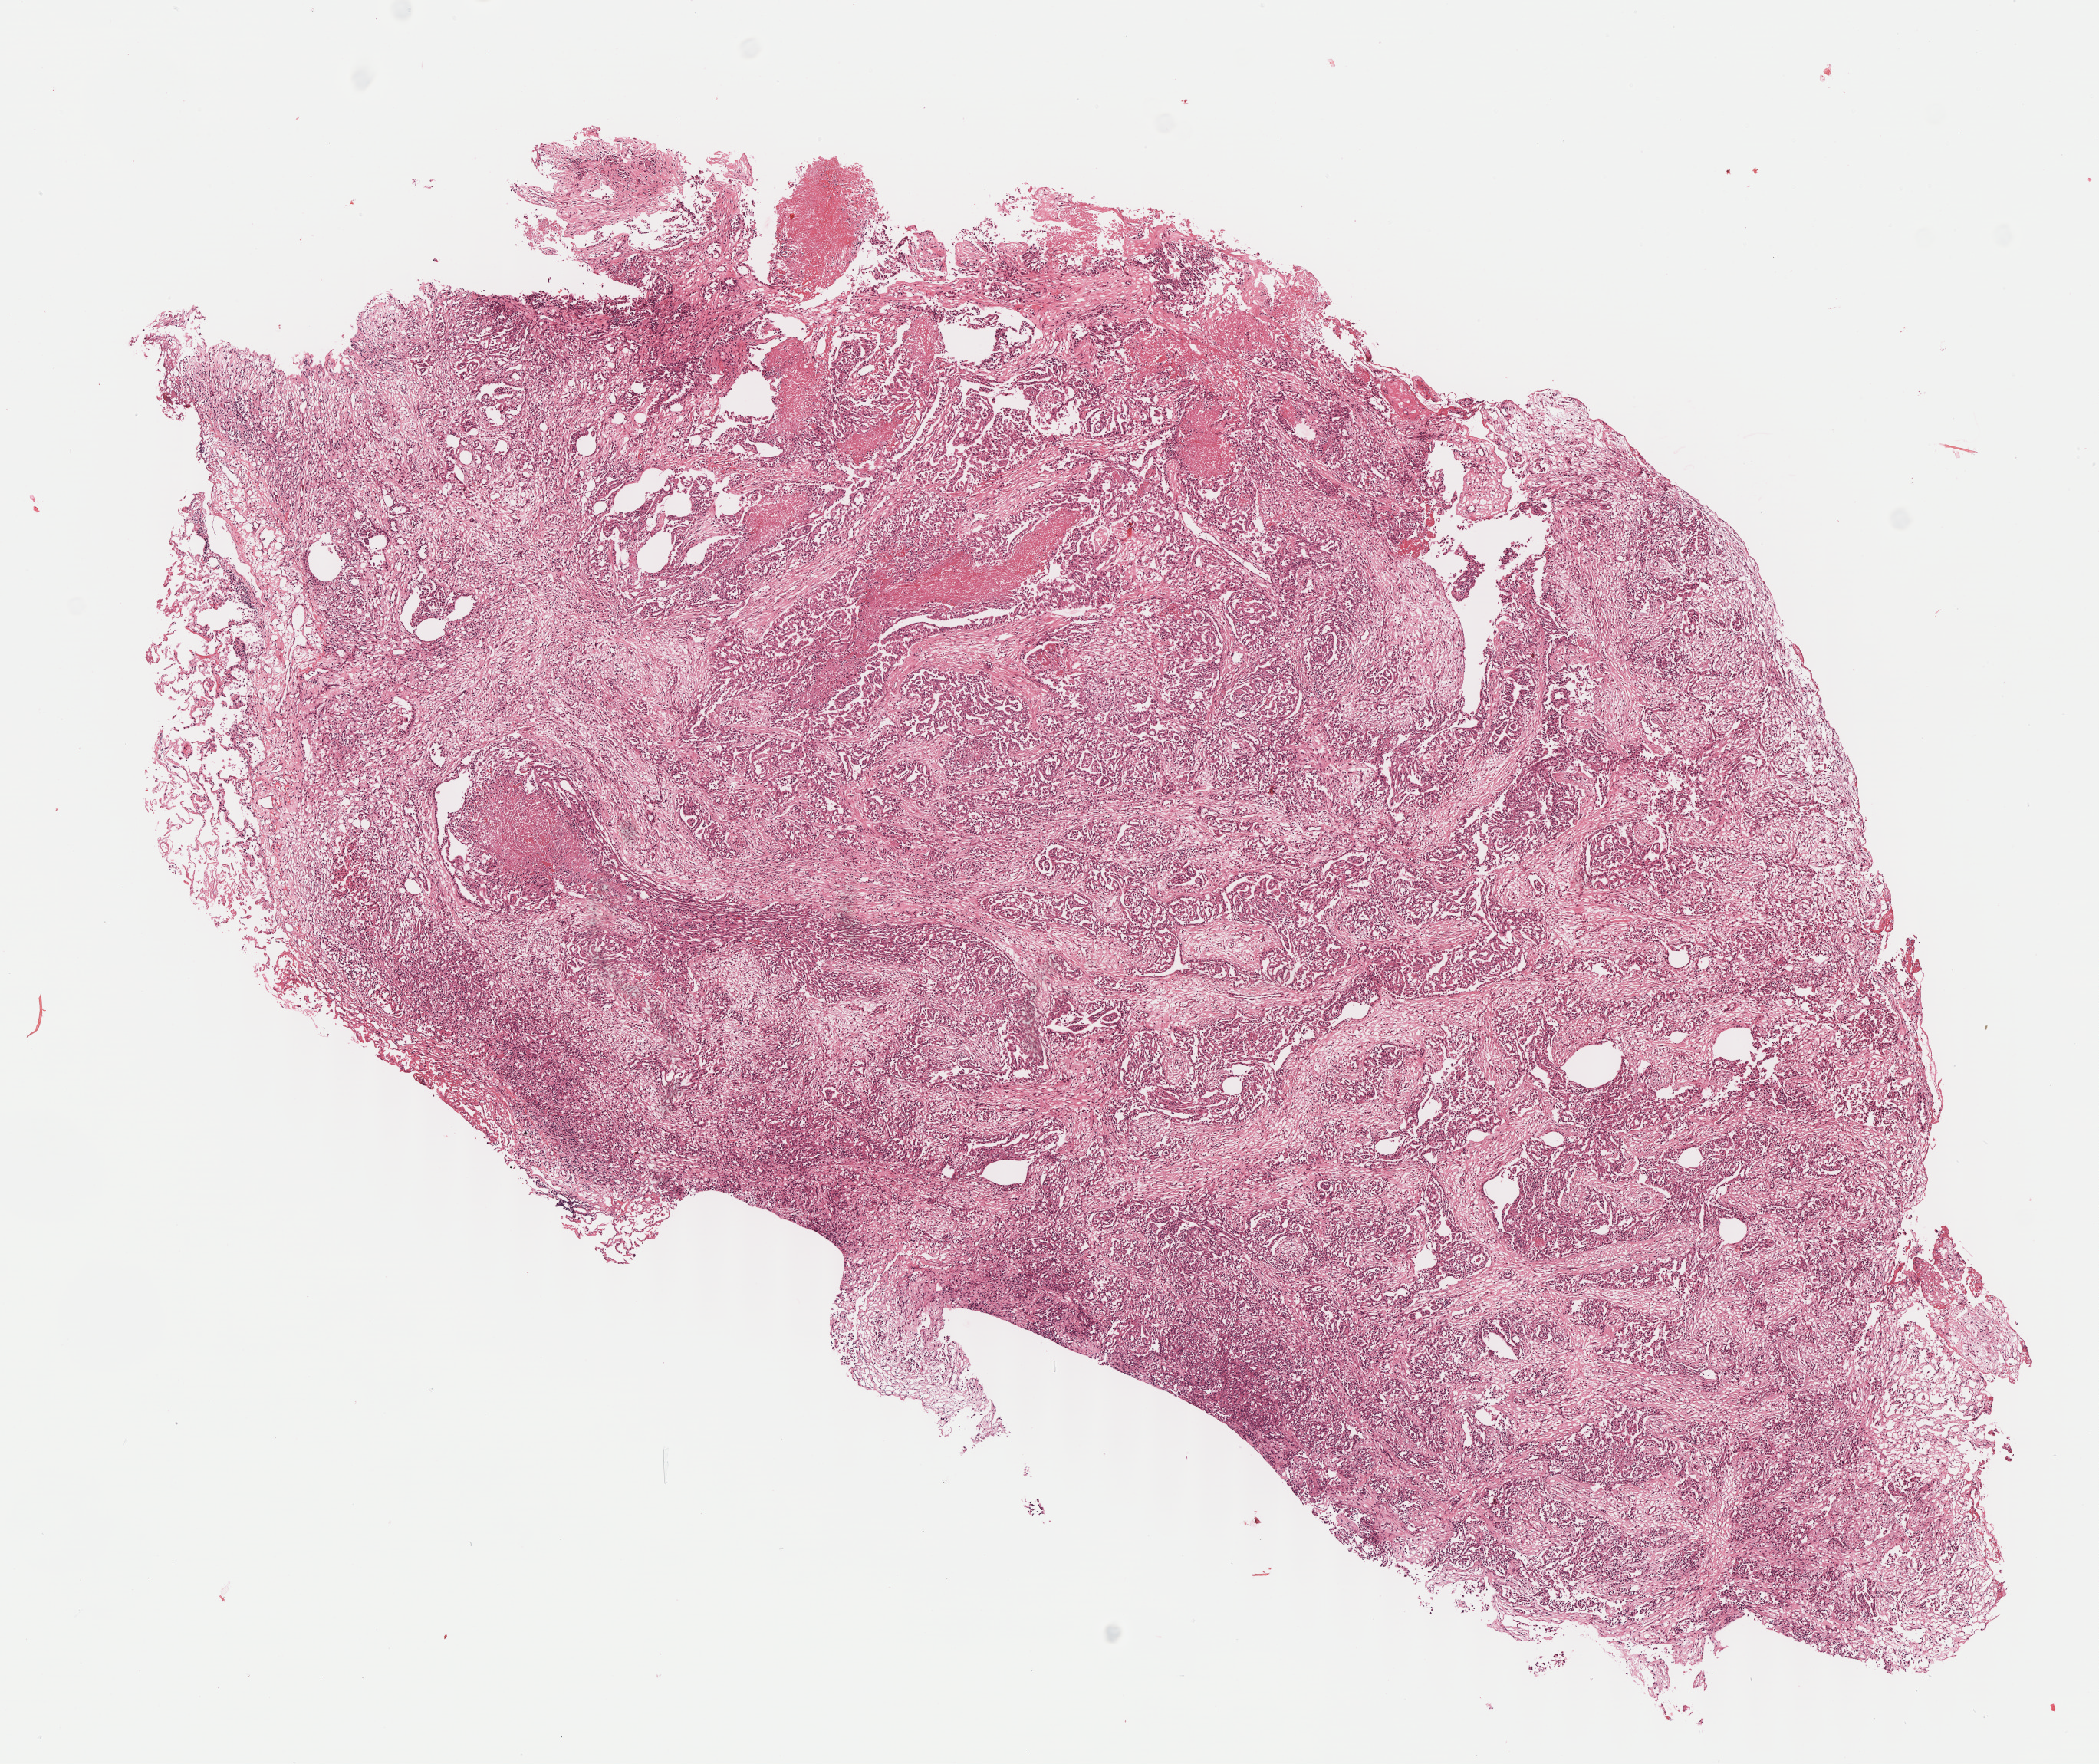
H&E whole-slide image, low-resolution overview of the scanned area, about 10.8 x 9.1 mm (slide scanned at 40x), formalin-fixed paraffin-embedded (FFPE) diagnostic section, mesothelium, primary tumour sample. Patient: male, age at initial diagnosis 46 years.
Diagnosis: Epithelioid mesothelioma, malignant. AJCC pathologic stage: II (6th edition).